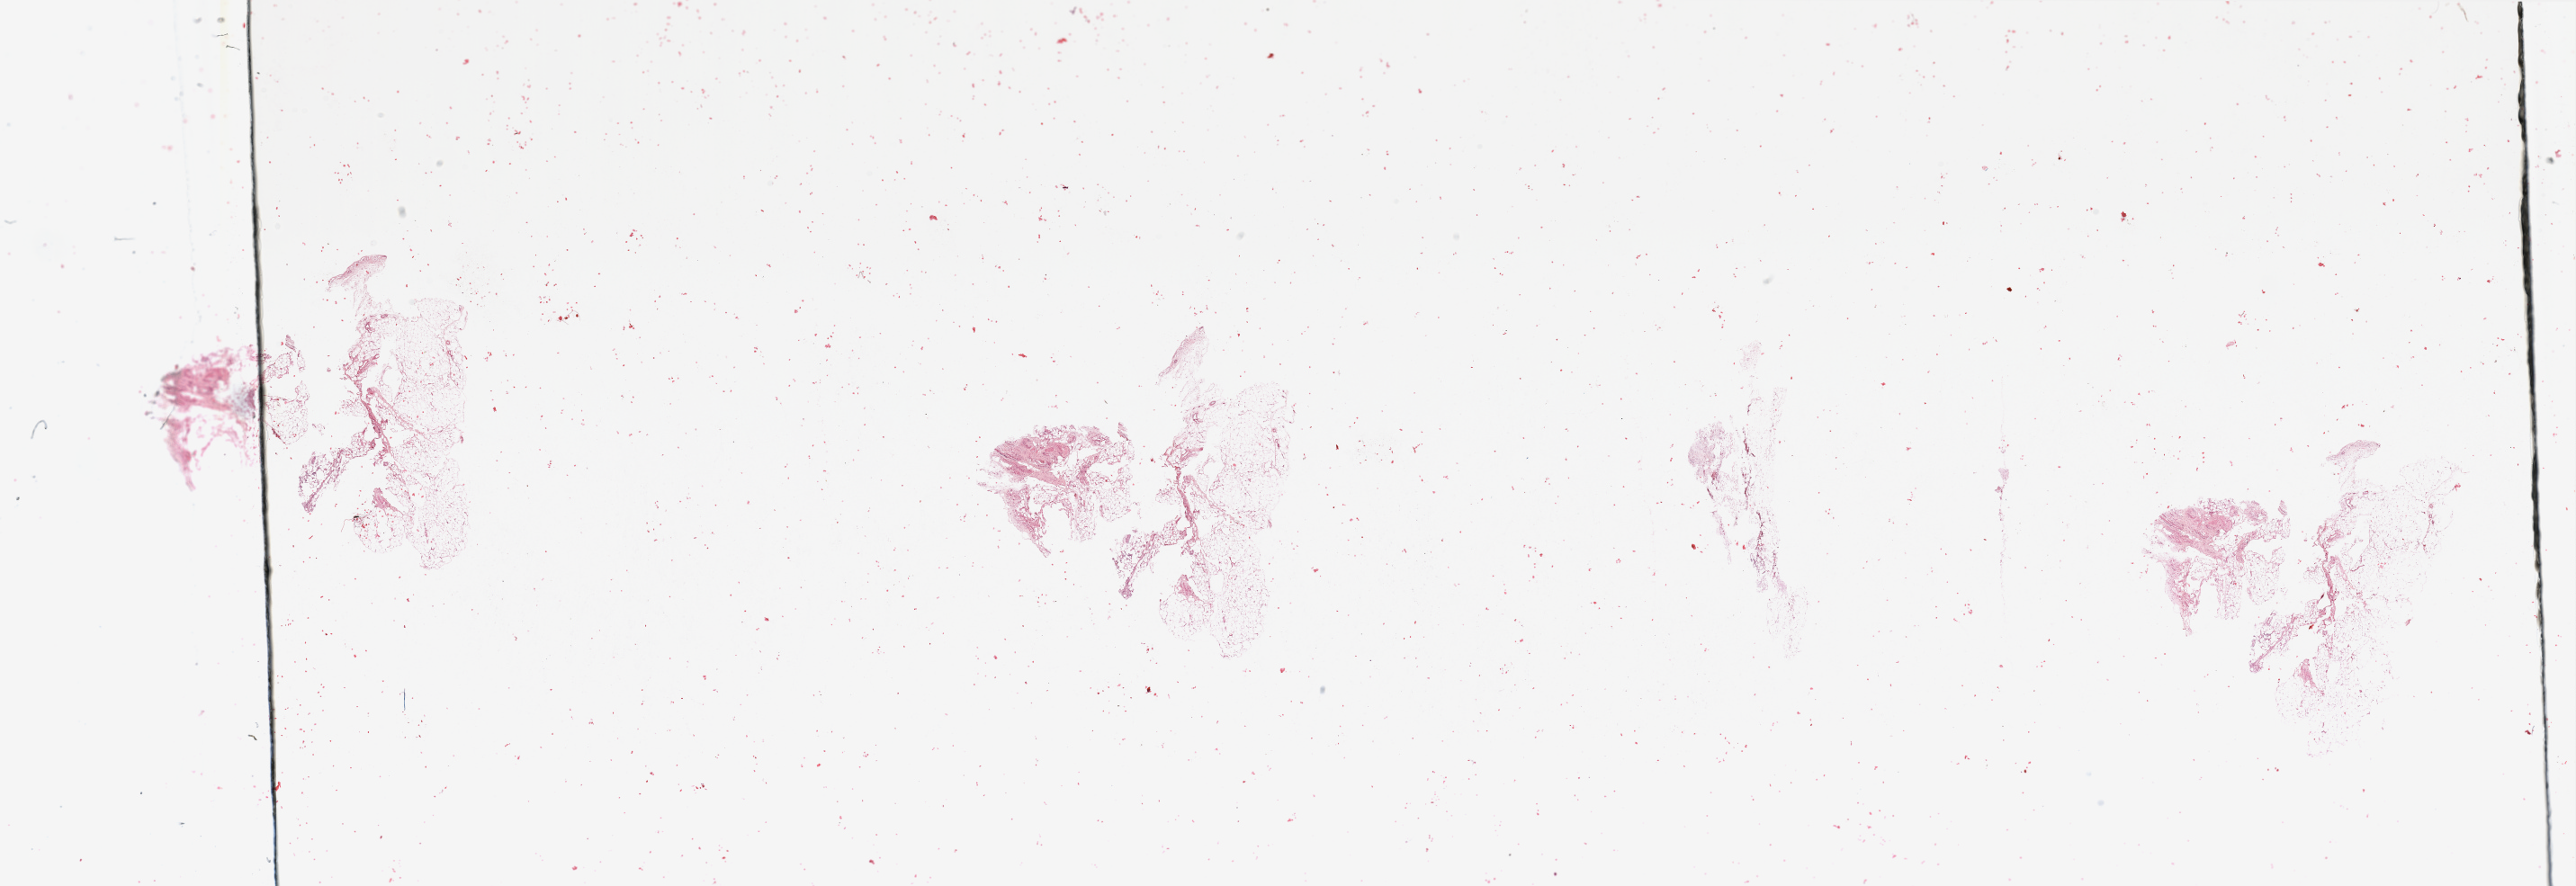
Hematoxylin and eosin (H&E) stained whole-slide image, low-resolution overview of the scanned area, about 45.3 x 15.6 mm (acquisition: 20x scan), pancreas, normal (non-tumour) tissue. Patient: female, age 63 years.
• this section: normal (non-tumour) tissue from the same patient
• patient diagnosis: Infiltrating duct carcinoma, NOS